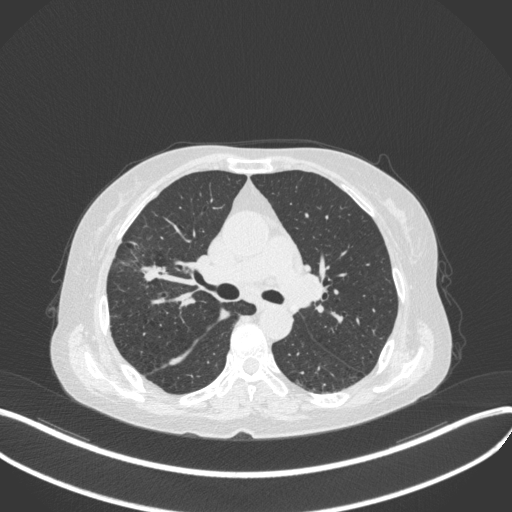
Chest CT, one axial slice; slice 250 of 429 in the series (ordered by position); reconstruction kernel B31f; 120 kVp; lung window (W 1500 / L -600 HU); 1 mm slice thickness; 512 × 512 image matrix, field of view 400 × 400 mm. Female patient, age 69 years. Case-level facts recorded for this patient, not image findings: clinical TNM (as recorded): T1b N3 M0.
Outlined on this slice (bounding box drawn by a radiologist):
- lung tumour (recorded histology: small cell carcinoma): box from (x=135, y=257) to (x=171, y=286) px